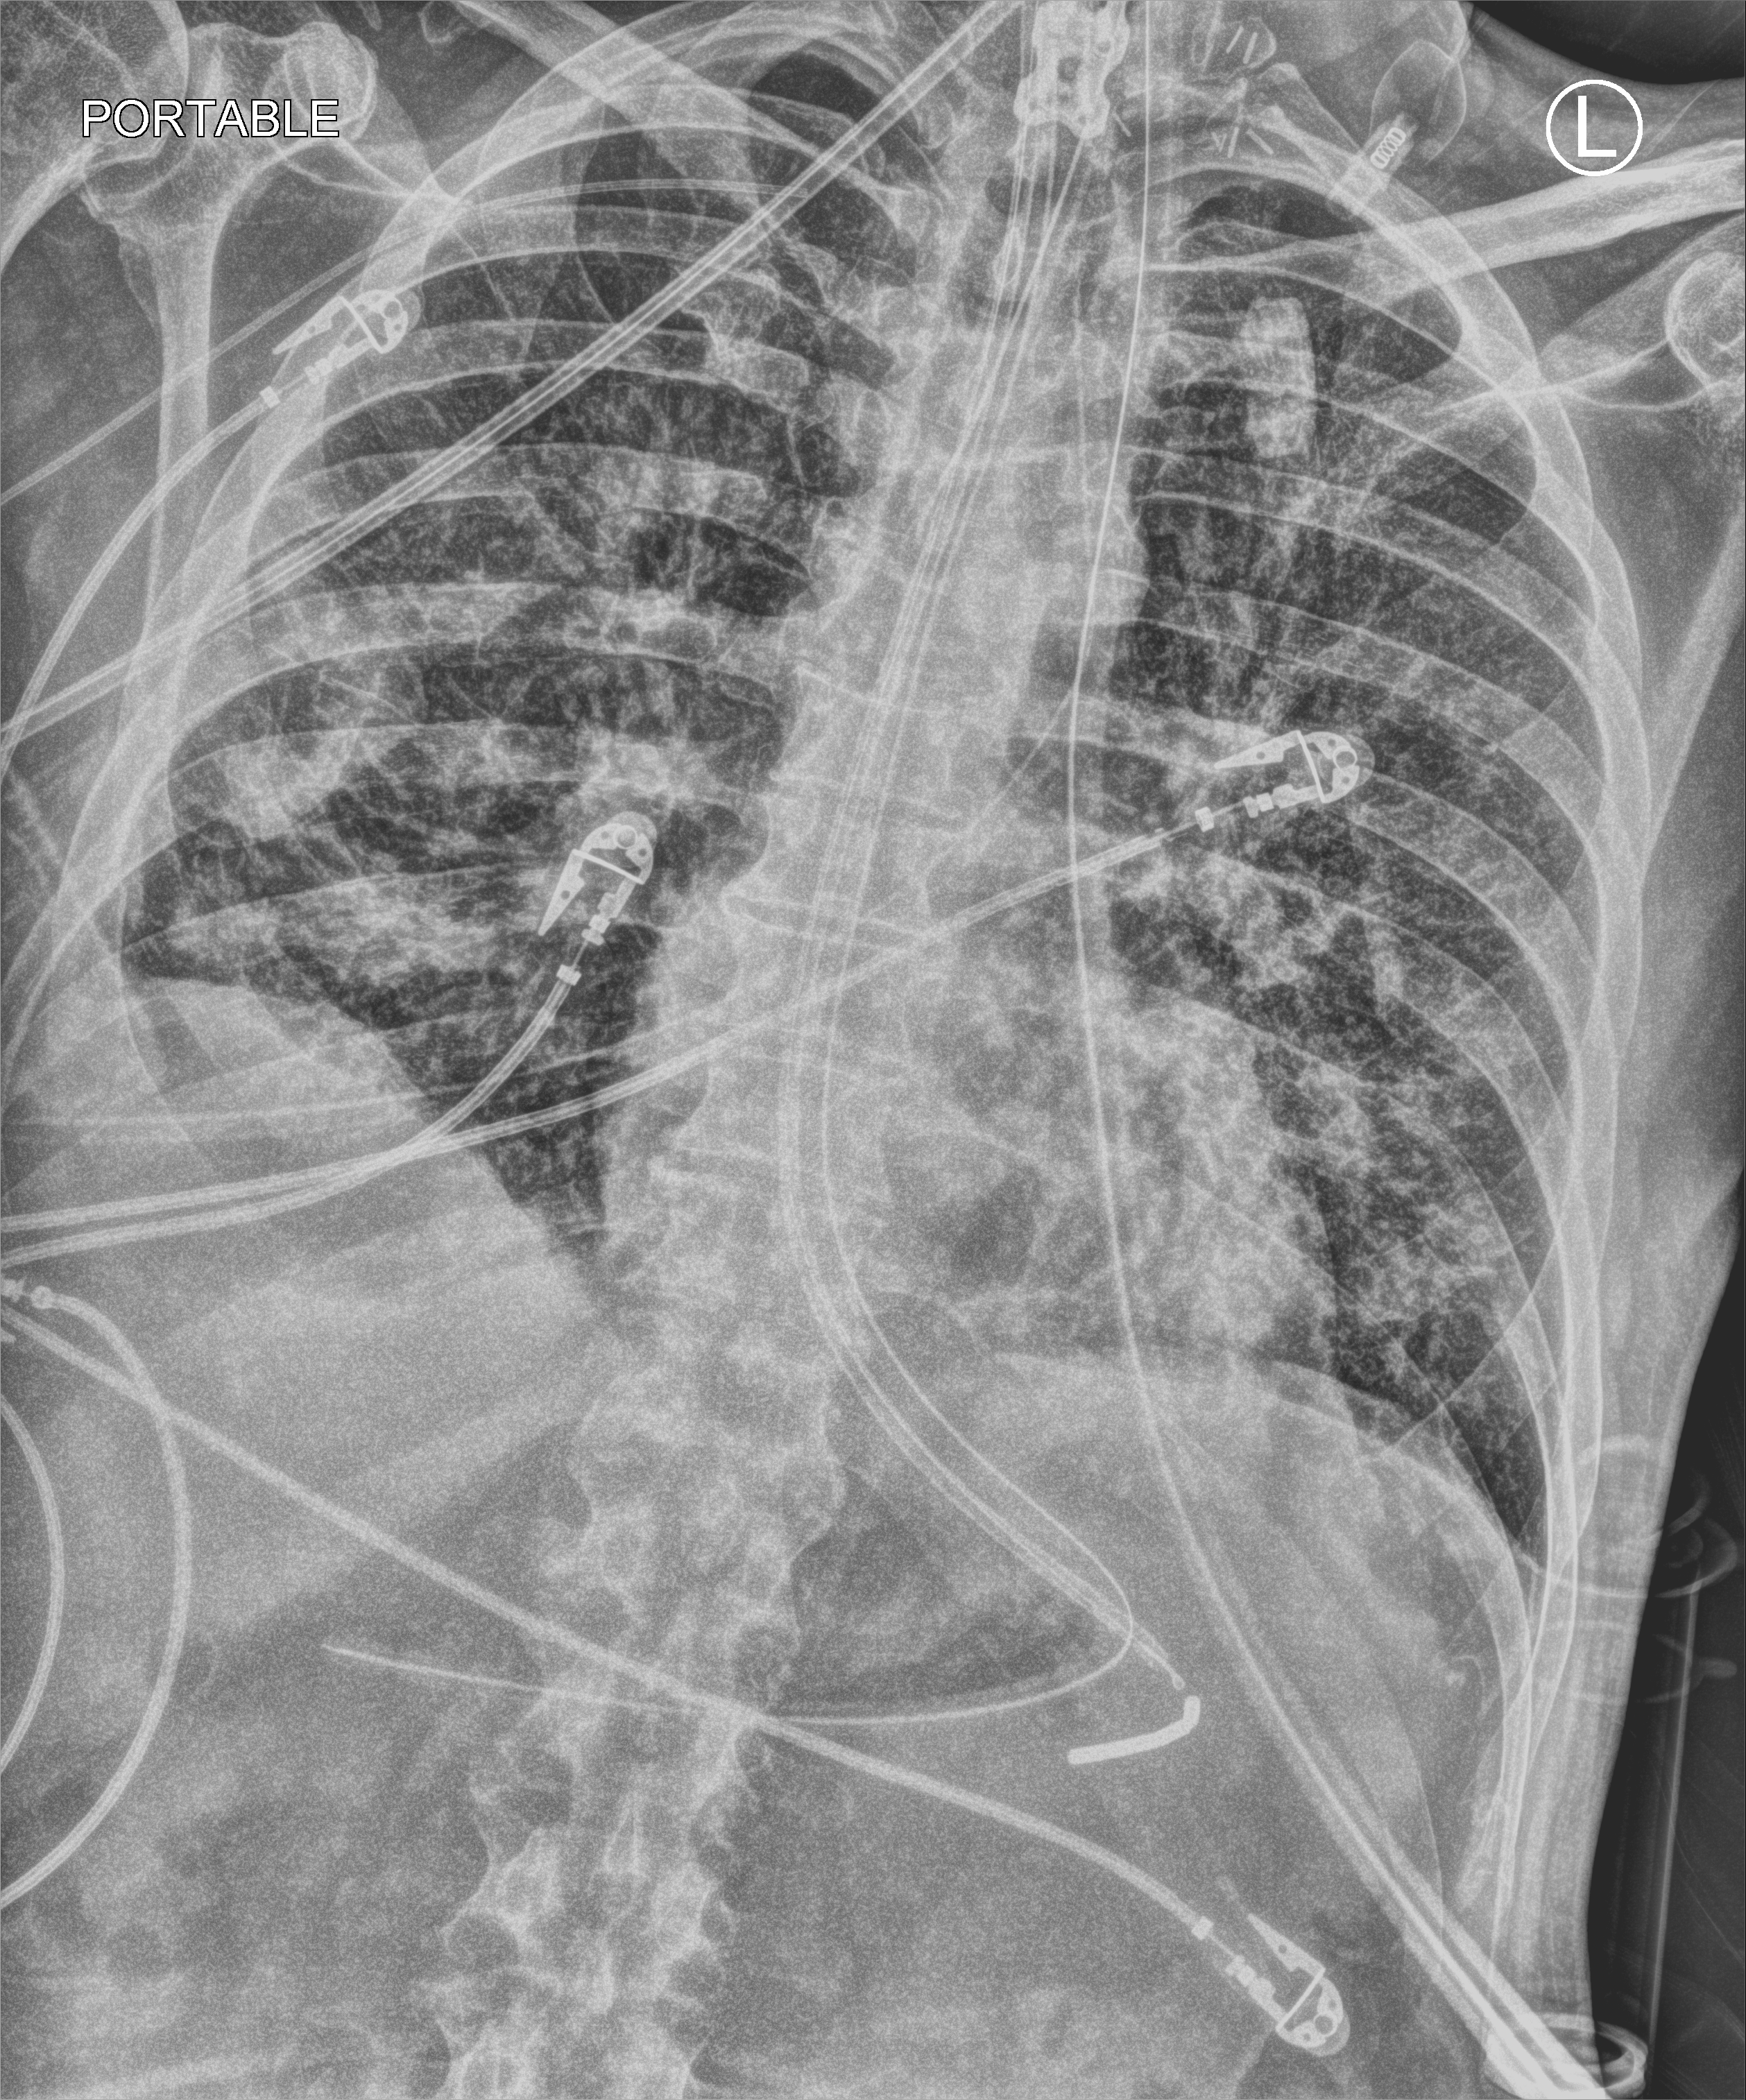
Portable chest radiograph, anteroposterior (AP) projection. Male patient hospitalised with COVID-19, age 60–74 years.
Hospital-stay facts (about this admission, not read from this image; timing relative to this image not recorded): mechanically ventilated during this hospital stay: yes; admitted to intensive care during this hospital stay: yes.